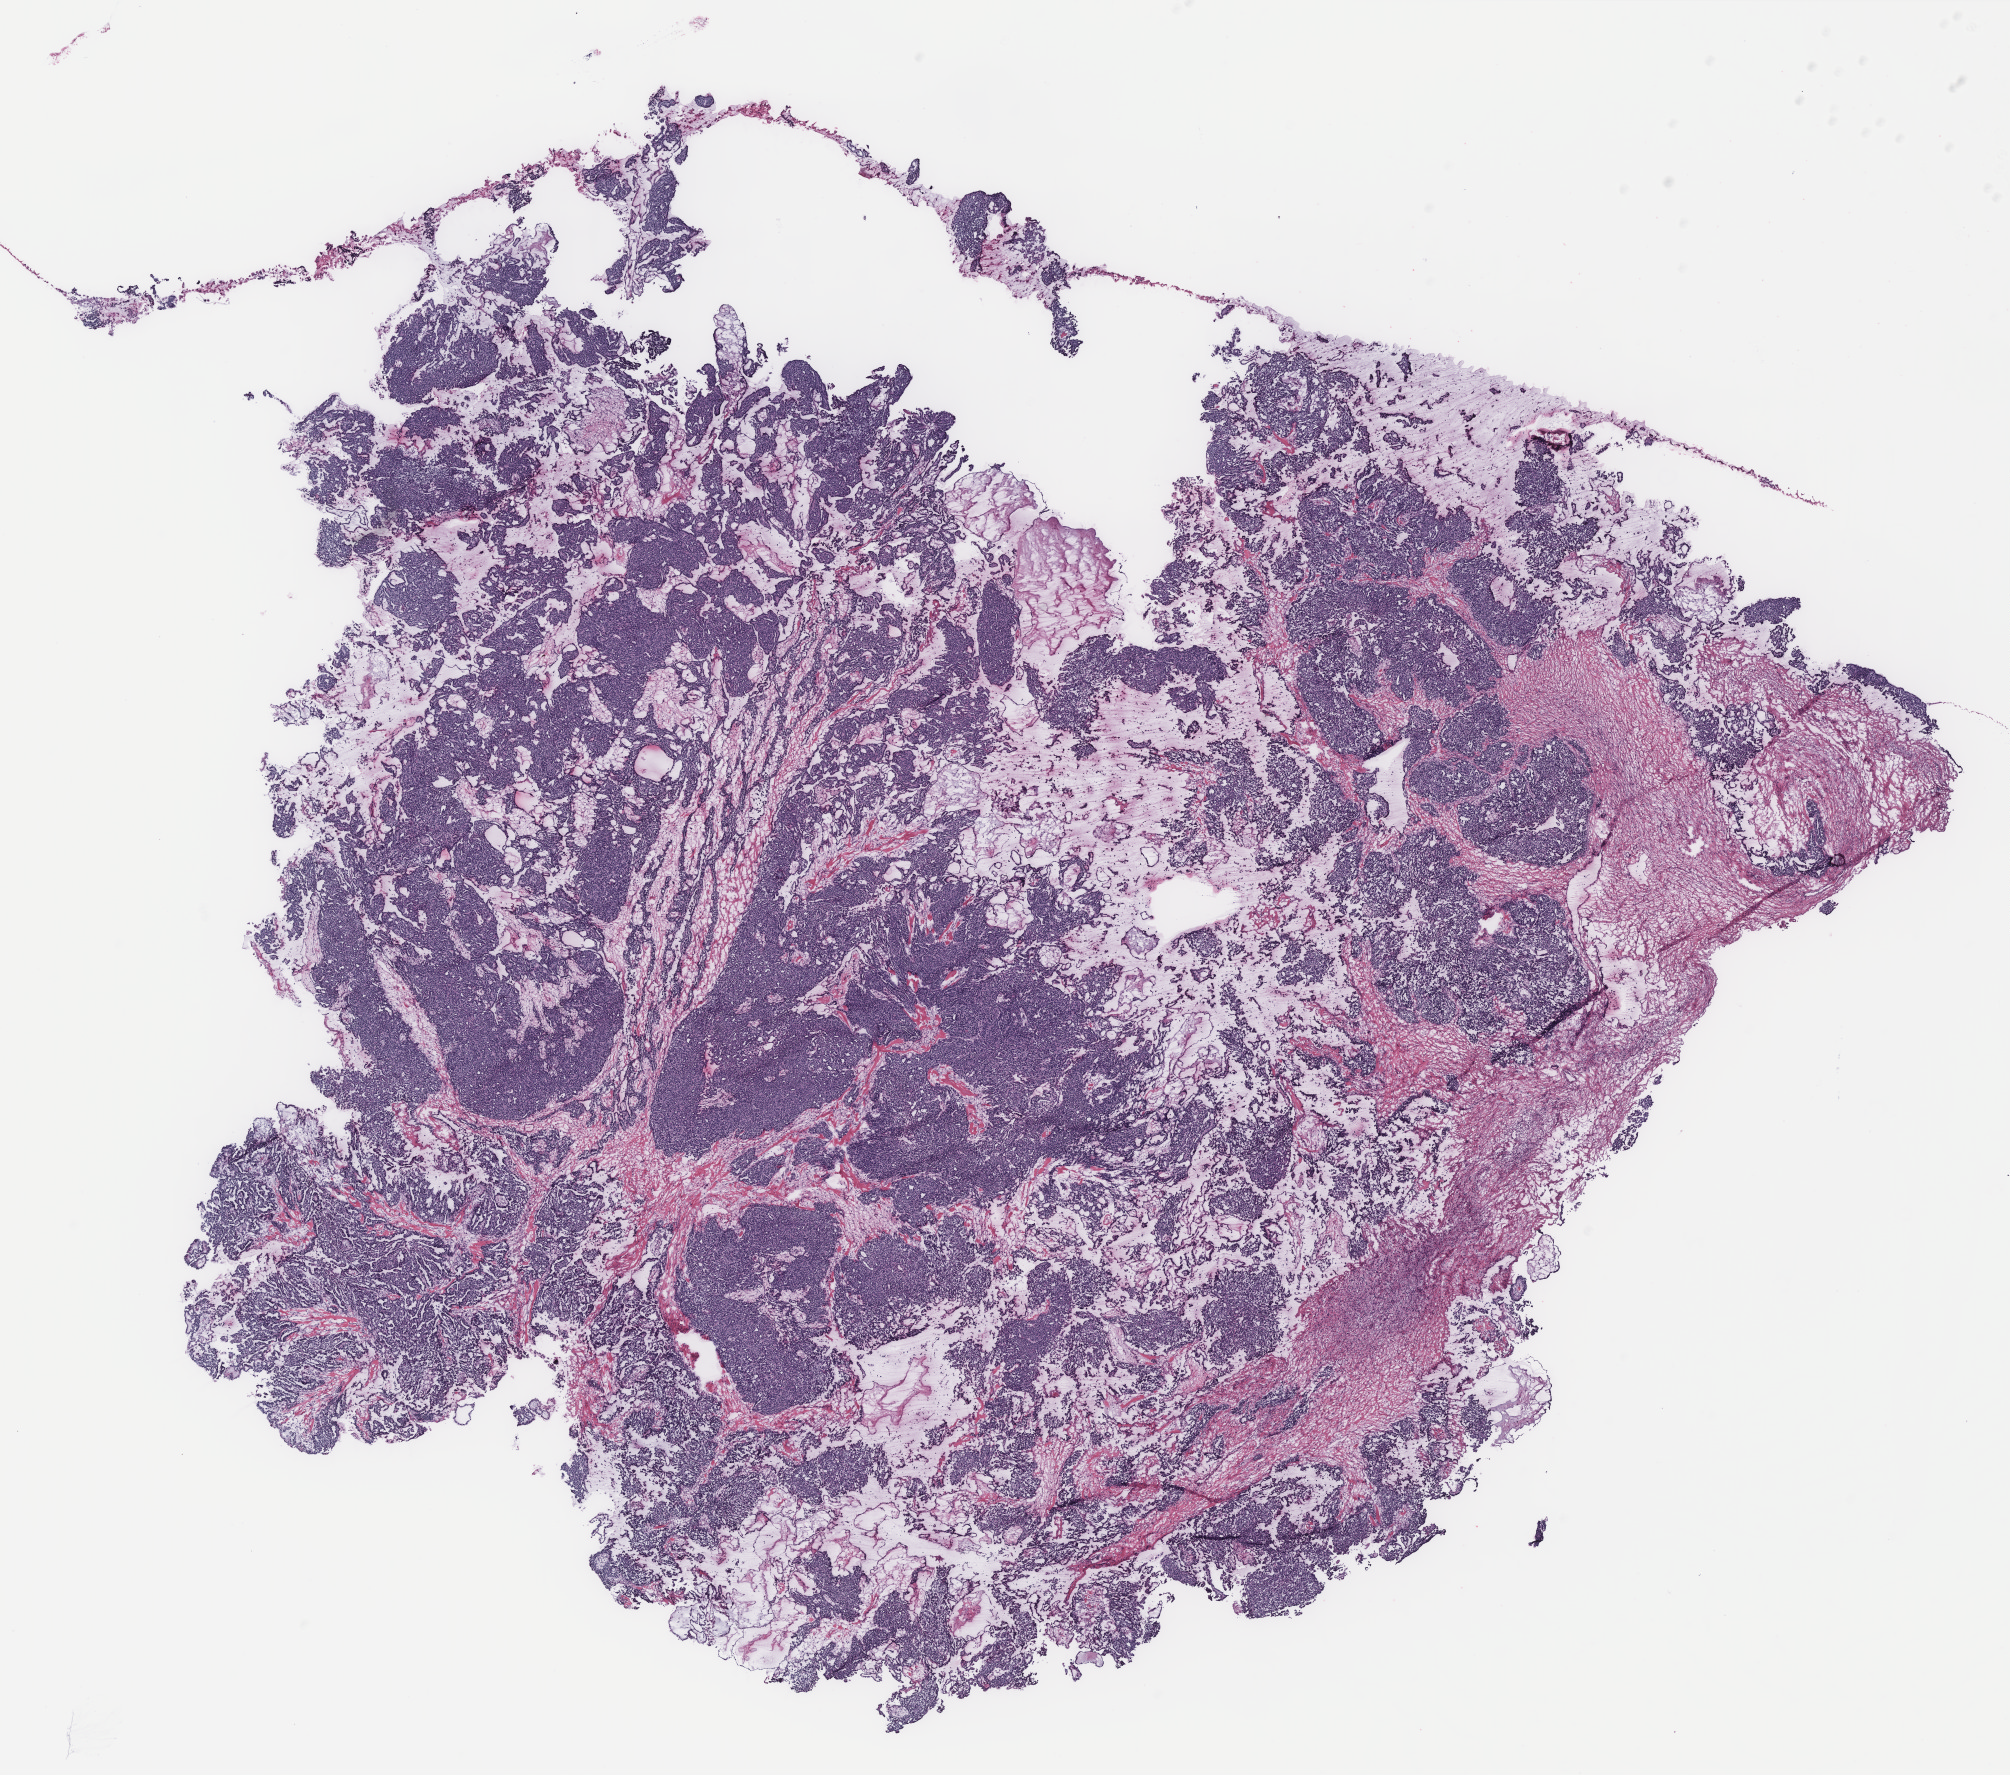
H&E whole-slide image — shown as a low-resolution overview of the whole scanned area (about 16.1 x 14.2 mm). Tumour tissue sample, ovary. 61-year-old female patient.
Diagnosis: Serous adenocarcinoma, NOS. Primary tumour site (as recorded): ovary.